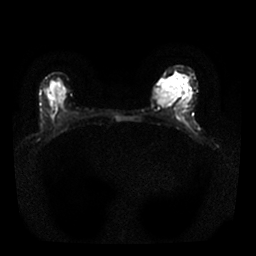
Breast MRI, one axial slice. Position 12 of 25 along the scan axis. Diffusion-weighted series; image 2 of 4 stored at this slice position (different b-values; order by instance number). 1.5 T. 4 mm slice thickness. 256 × 256 image matrix, field of view 310 × 310 mm. Female patient.
Structures marked on this image (expert manual segmentation):
- tumour on diffusion-weighted imaging: bounding box <155,78,178,106> (left, top, right, bottom; pixels)